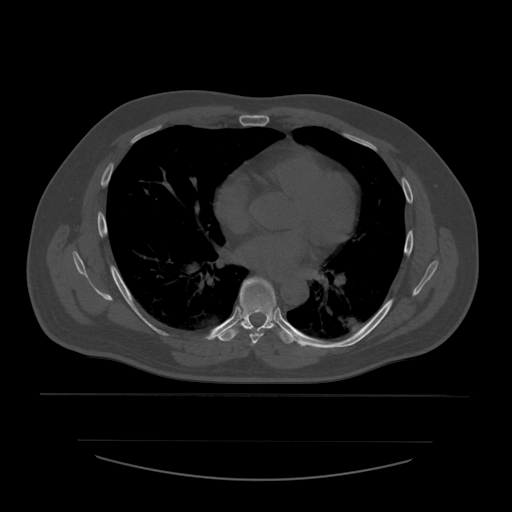
CT including the spine, one axial slice; position 367 of 532 along the scan axis; reconstruction kernel STANDARD; 120 kVp; bone window (W 1800 / L 400 HU); 512 × 512 image matrix, field of view 441 × 441 mm. Patient age 44 years. Case-level facts recorded for this patient, not image findings: primary cancer: soft tissue sarcoma.
Outlined on this slice (semi-automatically segmented with operator editing):
- T5 vertebra: bounding box (x1, y1, x2, y2) in pixels: (252, 343, 254, 345)
- T6 vertebra: (250, 278, 276, 345)
- T7 vertebra: (217, 278, 294, 344)